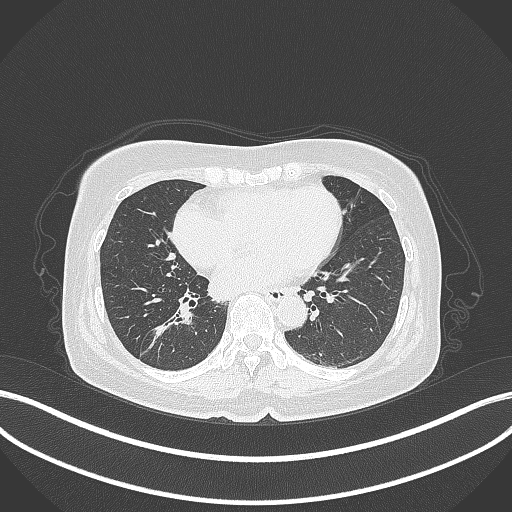
Chest CT, one axial slice. Position 165 of 429 along the scan axis. Reconstruction kernel B70f. 120 kVp. Lung window (W 1500 / L -600 HU). 1 mm slice thickness. 512 × 512 image matrix, field of view 400 × 400 mm. Female patient, age 67 years. From the clinical record (not read from this slice): clinical TNM (as recorded): T1c N1 M0; histopathological grade: G2-3.
Annotated regions visible in this slice (rectangle marked by the reading radiologist):
- lung tumour (recorded histology: adenocarcinoma): bounding box <135,304,193,353> (left, top, right, bottom; pixels)